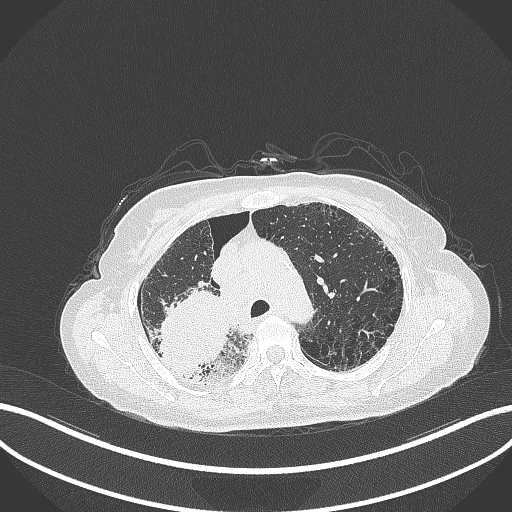
Chest CT, one axial slice; position 251 of 408 along the scan axis; reconstruction kernel B70f; 120 kVp; lung window (W 1500 / L -600 HU); 1 mm slice thickness; 512 × 512 image matrix, field of view 400 × 400 mm. Patient: female, 64 years. From the clinical record (not read from this slice): clinical TNM (as recorded): T3 N3 M0.
Outlined on this slice (bounding box drawn by a radiologist):
- lung tumour (recorded histology: squamous cell carcinoma): bounding box [x1, y1, x2, y2] px = [152, 289, 230, 378]